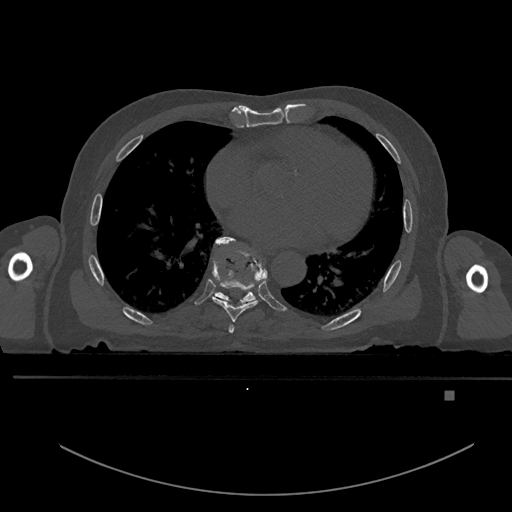
CT including the spine, one axial slice. Slice 236 of 969 in the series (ordered by position). Bone window (W 1800 / L 400 HU). 512 × 512 image matrix, field of view 456 × 456 mm. Patient: male, 82 years. Case-level facts recorded for this patient, not image findings: primary cancer: prostate; vertebrae with lytic lesions (as recorded): T11, T9, T8, T2.
Structures marked on this image (semi-automatic segmentation, software-assisted and operator-edited):
- T6 vertebra: bounding box <228,324,234,333> (left, top, right, bottom; pixels)
- T7 vertebra: <212,236,268,322>
- T8 vertebra: <211,239,259,305>